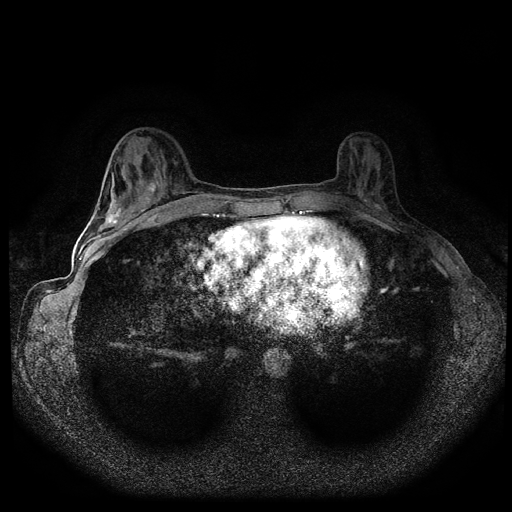
Breast MRI (dynamic contrast-enhanced, multi-phase), one axial slice; position 37 of 108 along the scan axis; dynamic contrast-enhanced series, time point 2 of 5 at this slice position (early post-contrast); 1.5 T; TE 2.7 ms, TR 5.5 ms; 512 × 512 image matrix, field of view 320 × 320 mm. Patient: female, 36 years.
Outlined on this slice (semi-automatically segmented with operator editing):
- breast lesion (labelled benign in the annotation): box from (x=144, y=179) to (x=161, y=195) px
- breast lesion (labelled benign in the annotation): (x=102, y=208)–(x=122, y=229)